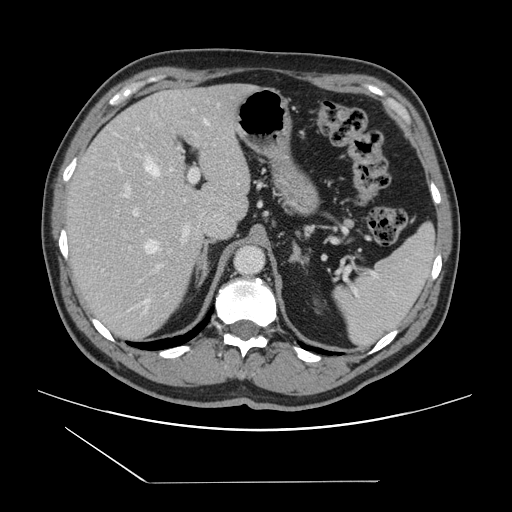
Contrast-enhanced abdominal CT, one axial slice. Position 98 of 157 along the scan axis. Intravenous contrast given. Soft-tissue window (W 400 / L 40 HU). 2.5 mm slice thickness. 512 × 512 image matrix. Male patient, age 61 years. From the clinical record (not read from this slice): diagnosis: colorectal cancer liver metastases, imaged before liver resection; multiple liver metastases: yes; largest metastasis: 5.5 cm; disease in both lobes: yes.
Outlined on this slice (manually delineated by an expert):
- hepatic veins: bounding box [x1, y1, x2, y2] px = [144, 119, 209, 302]
- liver: [66, 85, 250, 341]
- planned liver remnant (the part of the liver to remain after resection): [68, 85, 238, 223]
- portal vein (with intrahepatic branches): [119, 167, 199, 268]